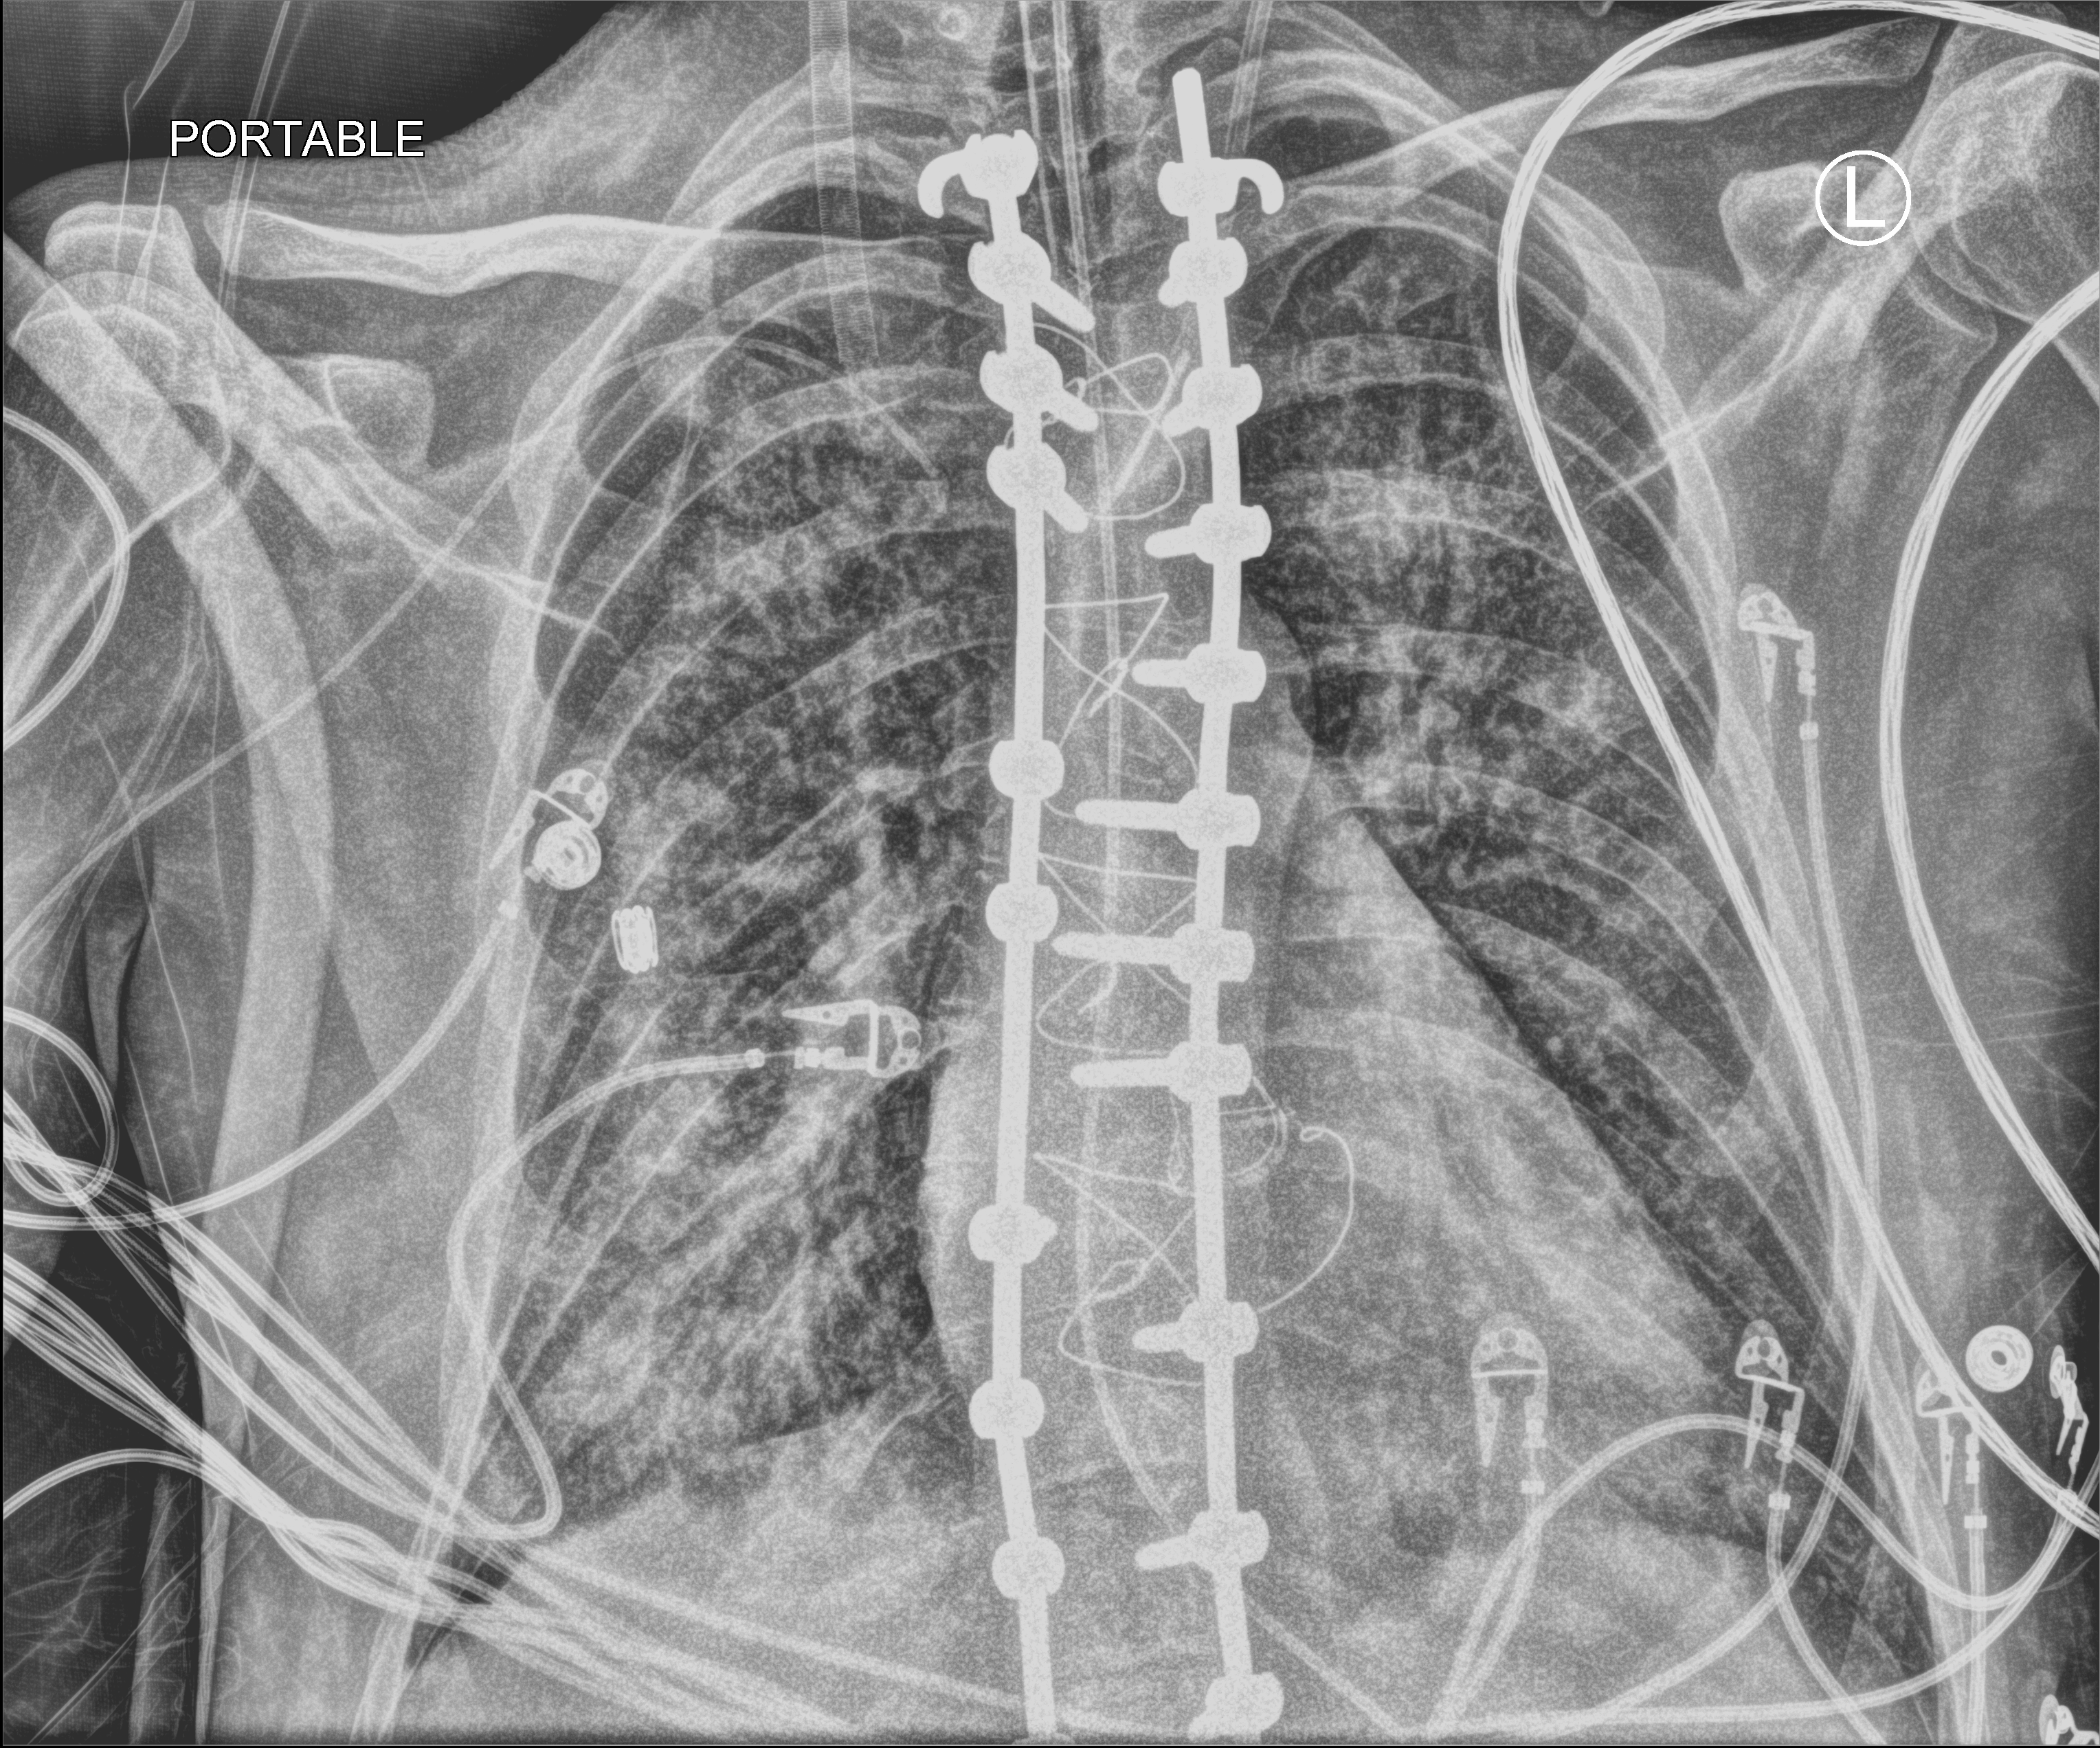
Portable chest radiograph; anteroposterior (AP) projection. Adult patient hospitalised with COVID-19, age 18–59 years.
From the hospital-stay record, not from the radiograph (when in the stay this image was taken is not recorded):
- admitted to intensive care during this hospital stay: yes
- chronic kidney disease (admission record): no